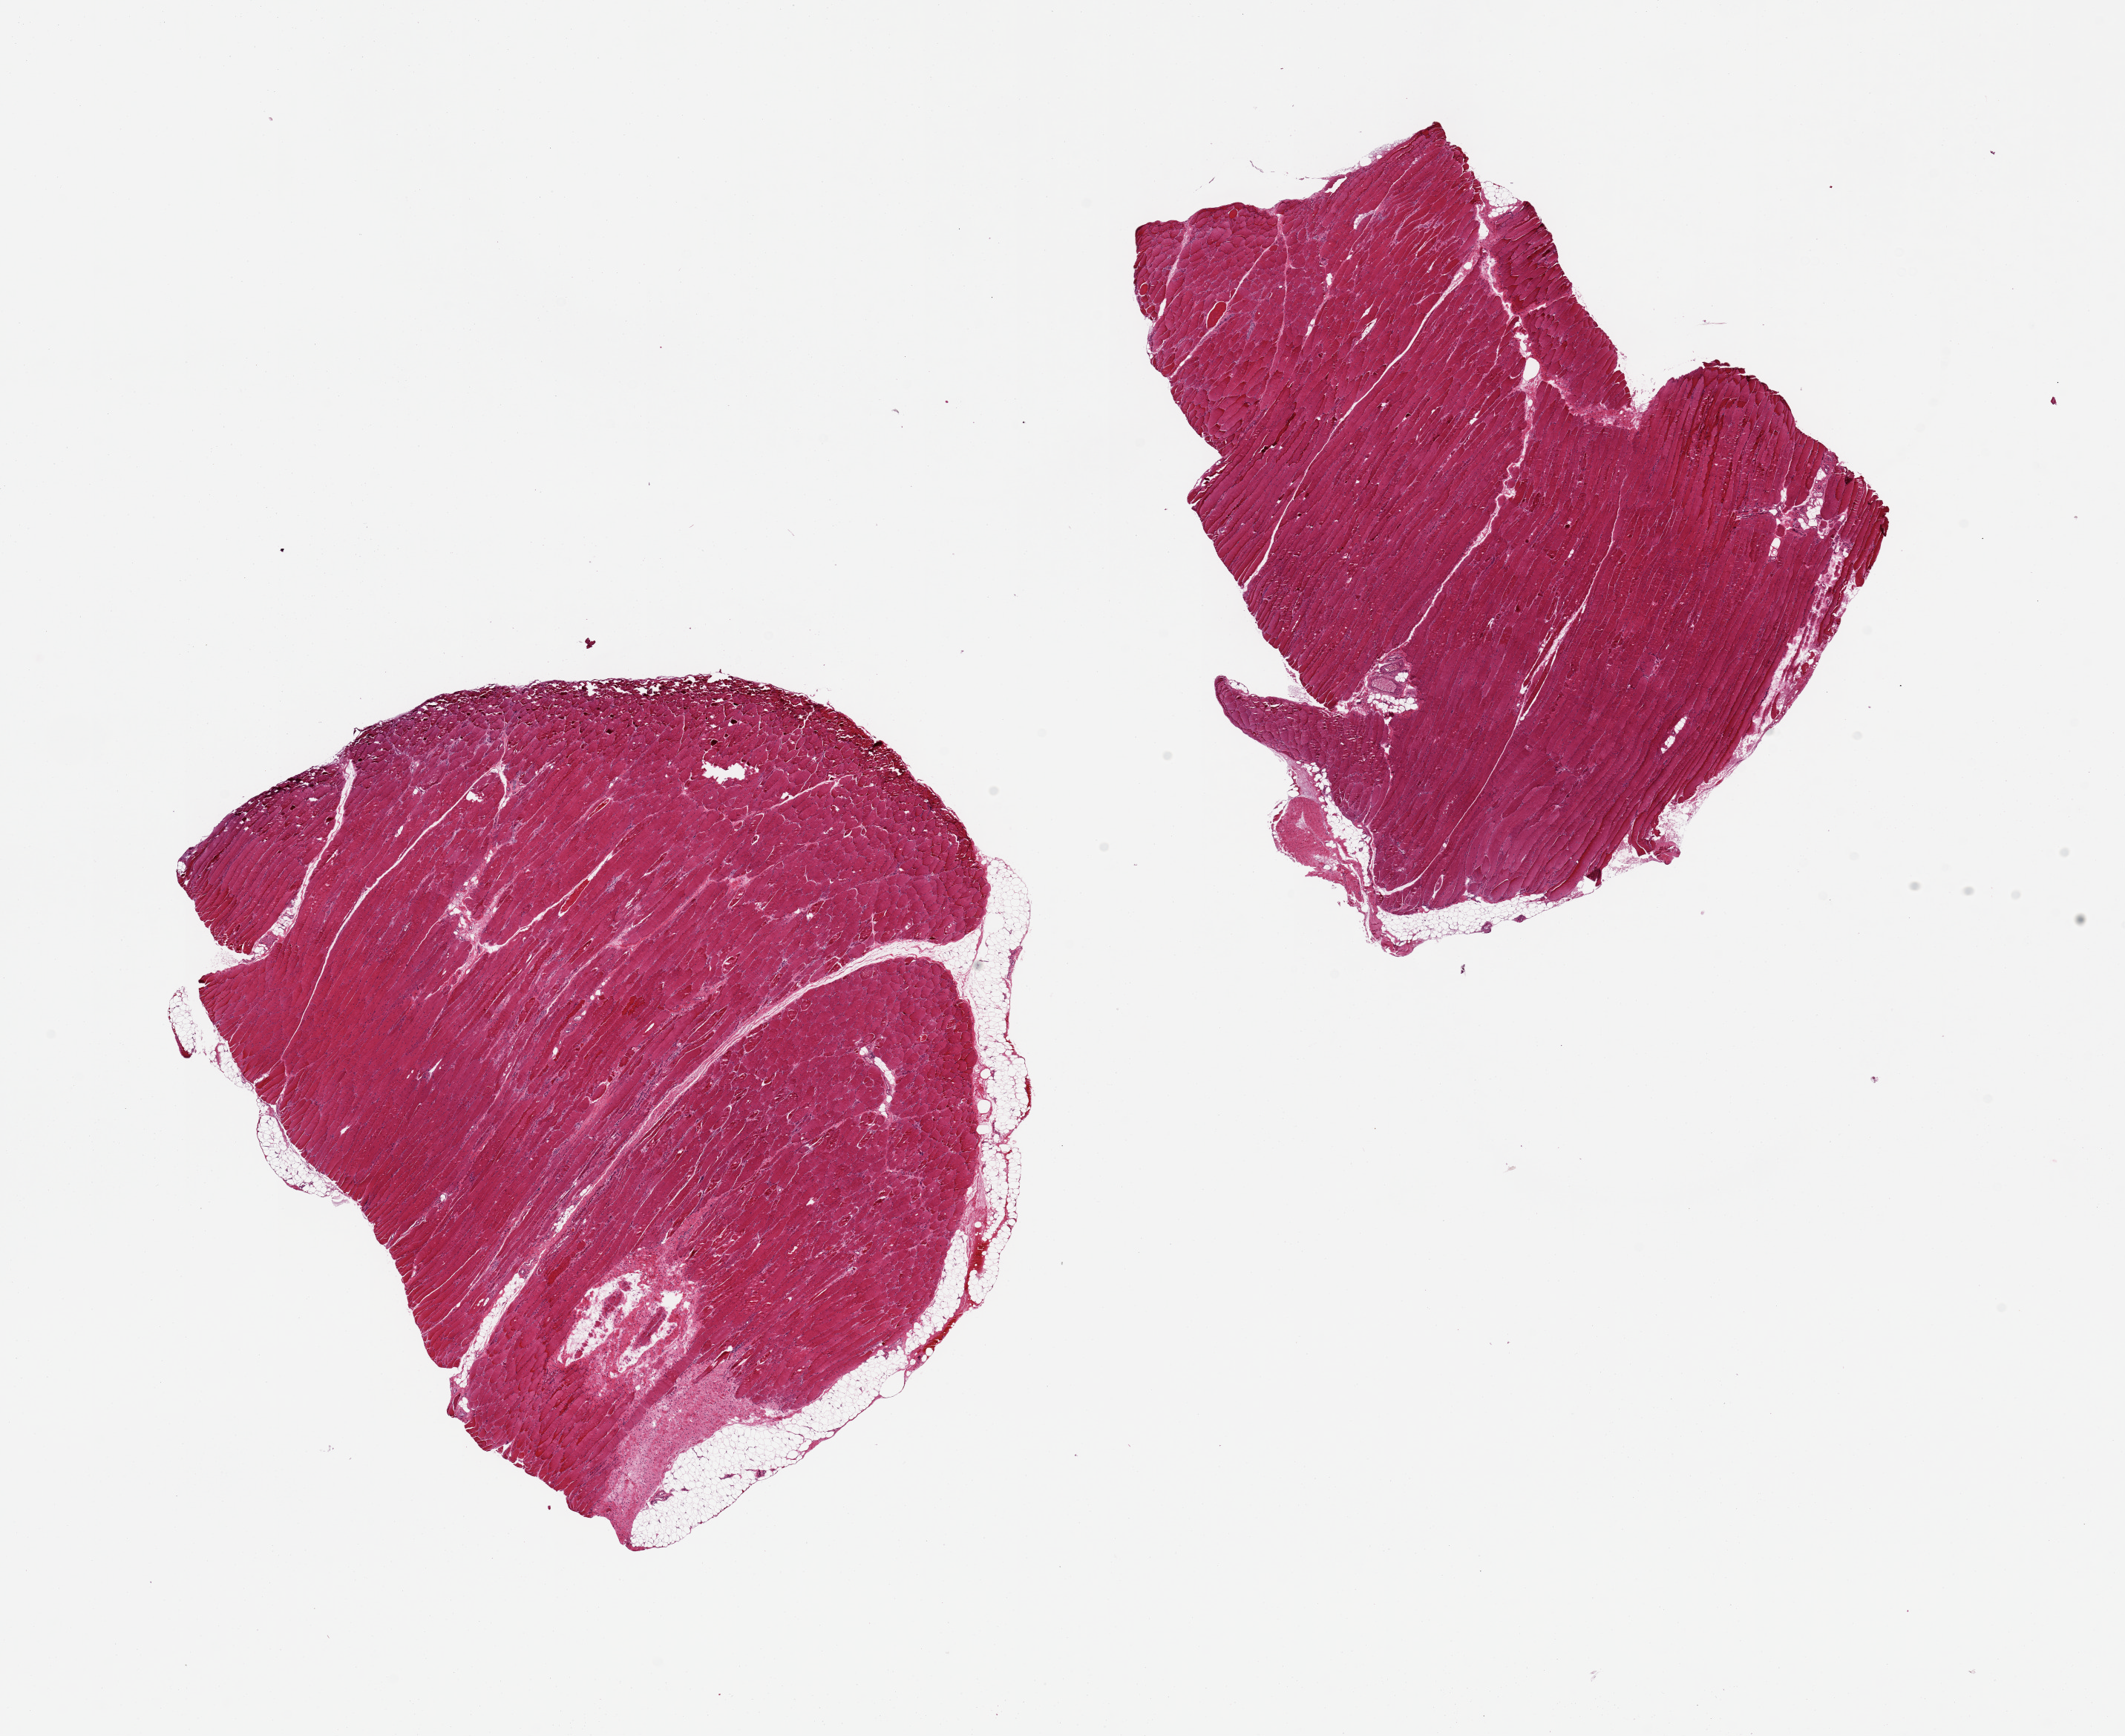
Whole-slide image, hematoxylin and eosin (H&E) stain, a low-resolution overview of the entire scanned area, about 22.6 x 18.5 mm (acquisition: 20x scan). PAXgene-fixed paraffin-embedded (PFPE) section. Target tissue: skeletal muscle. Donor tissue sample.
Review note (as recorded): 2 pieces, 9x9 & 9x7mm; <1% interstitial fat.